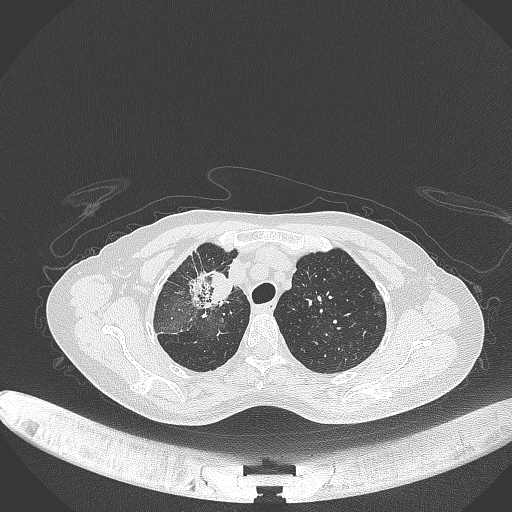
Chest CT, one axial slice. Slice 257 of 284 in the series (ordered by position). Reconstruction kernel B70f. 120 kVp. Lung window (W 1500 / L -600 HU). 1 mm slice thickness. 512 × 512 image matrix, field of view 400 × 400 mm. Female patient, age 59 years. Case-level facts recorded for this patient, not image findings: clinical TNM (as recorded): T3 N0 M0; histopathological grade: G1.
Structures marked on this image (bounding box drawn by a radiologist):
- lung tumour (recorded histology: adenocarcinoma): box from (x=187, y=266) to (x=233, y=308) px